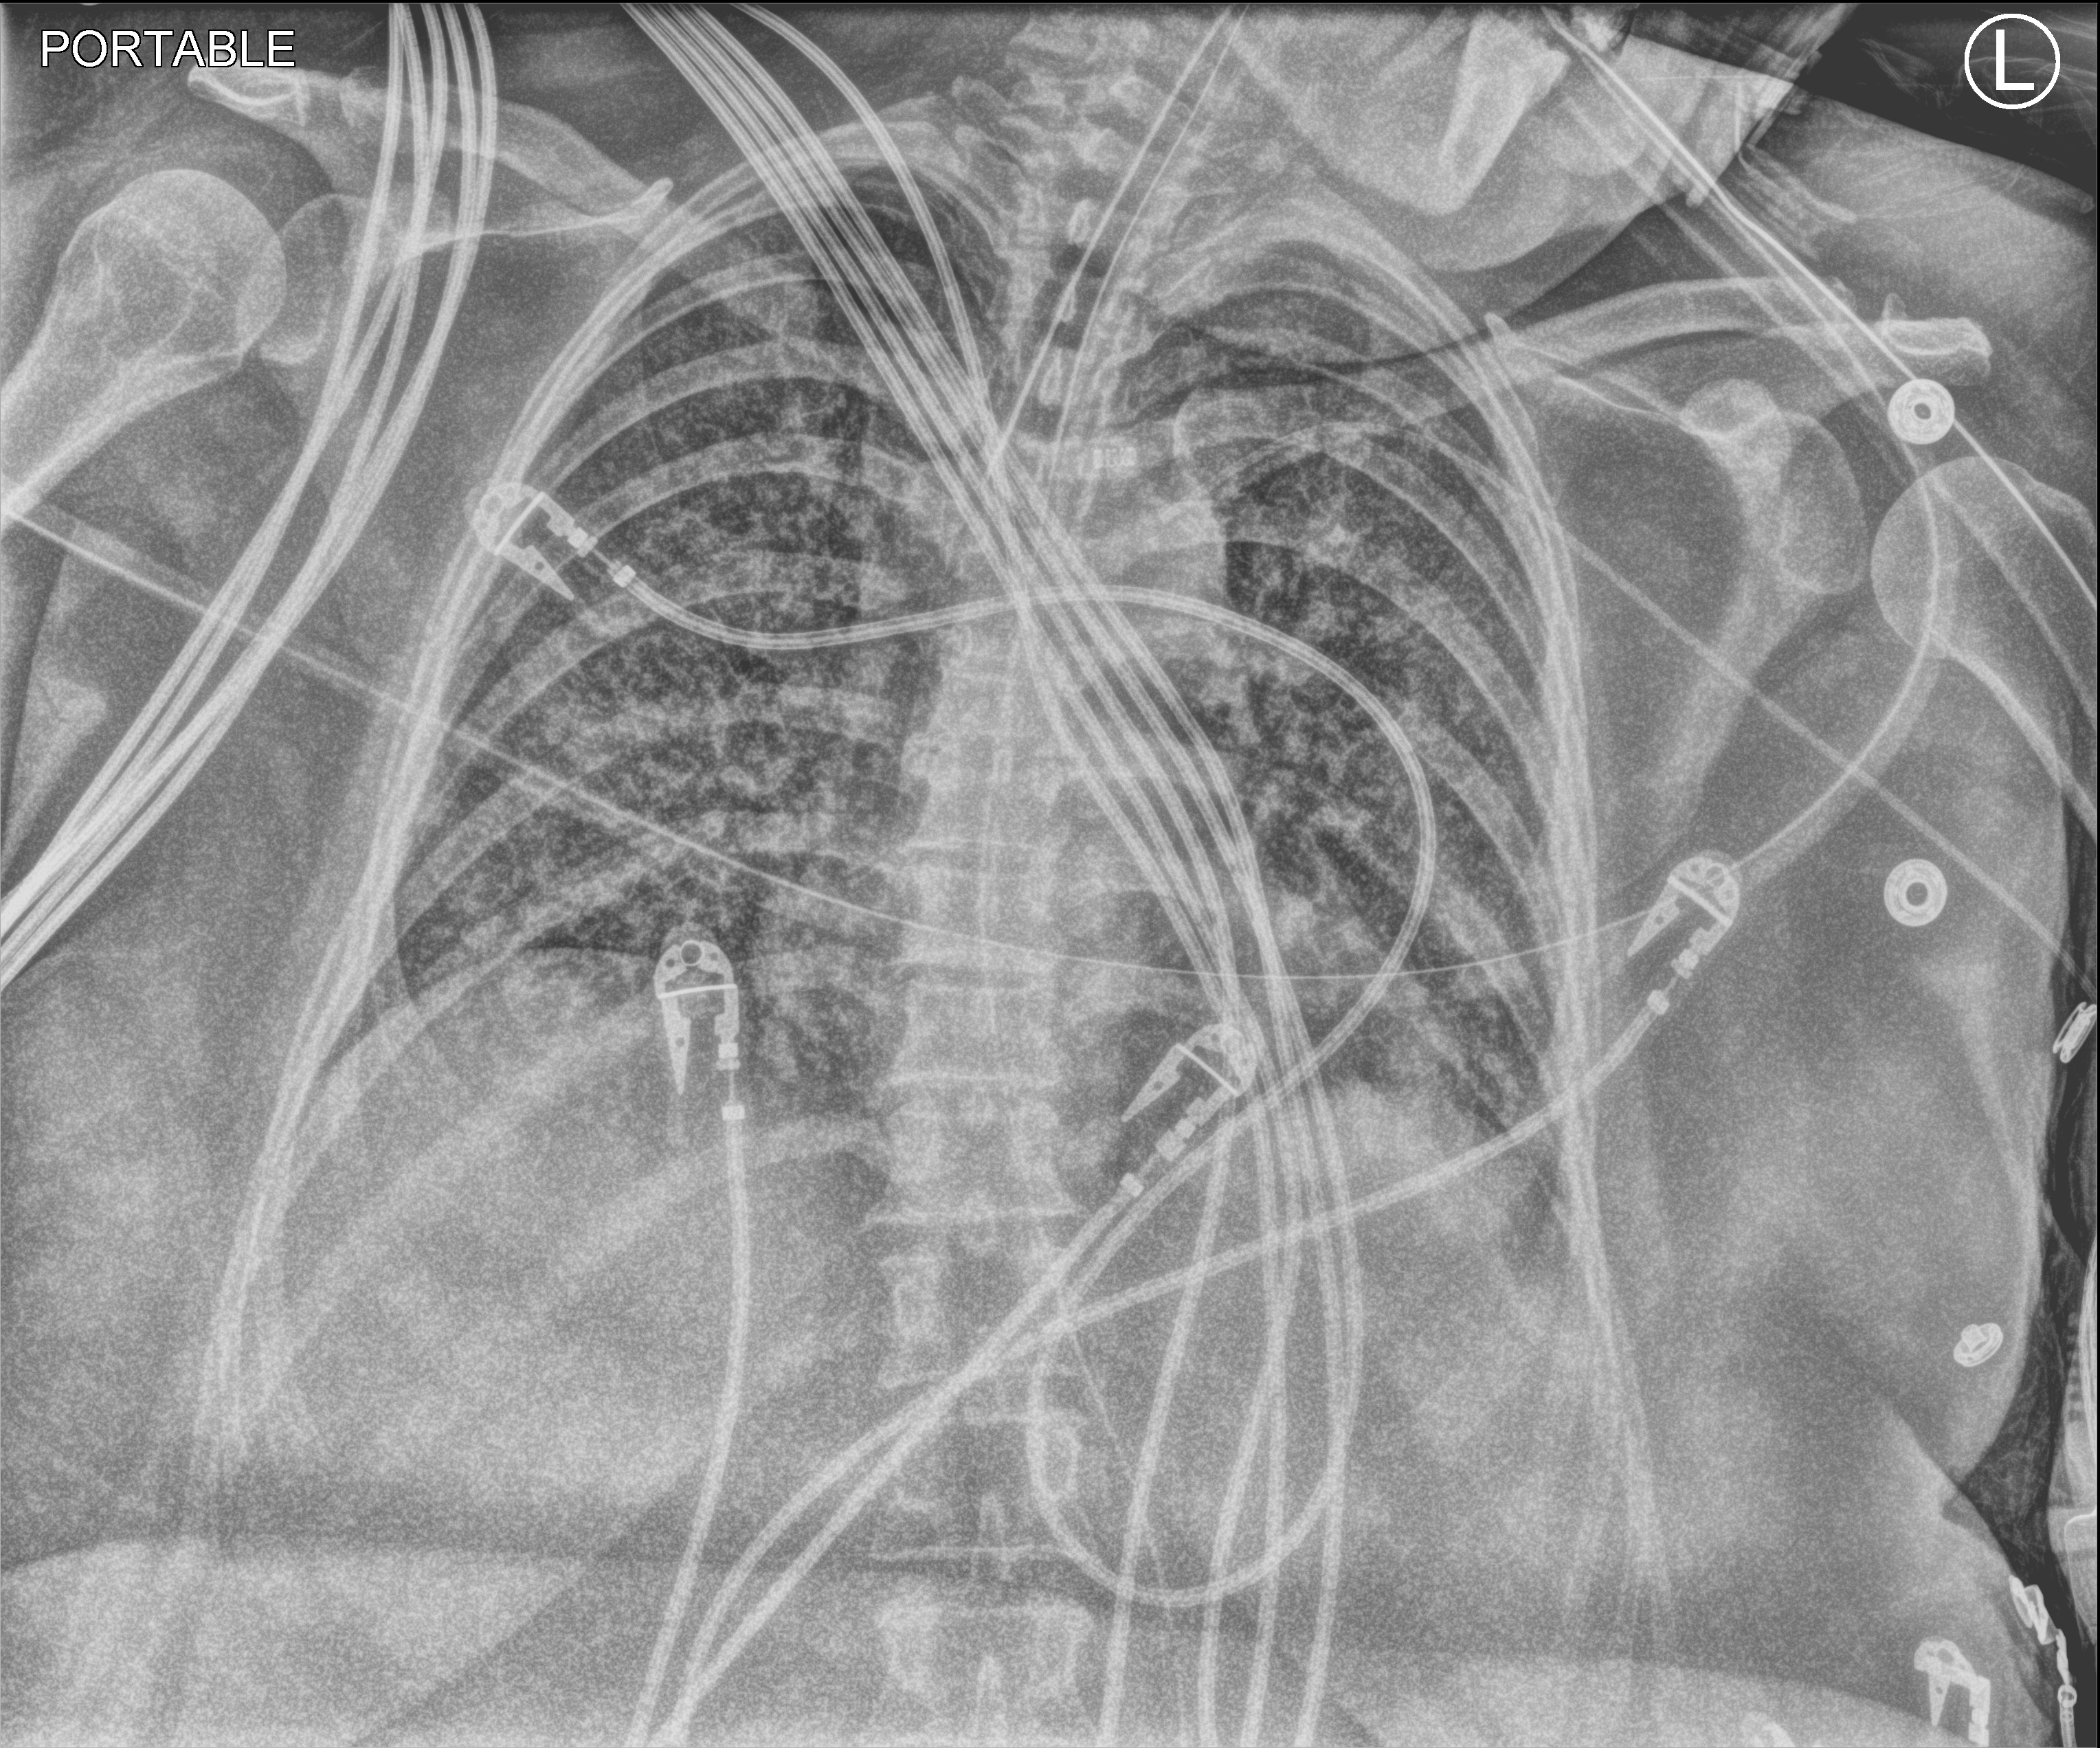
Chest X-ray (portable); anteroposterior (AP) projection. Patient hospitalised with COVID-19; female, aged 18–59 years.
Hospital-stay facts (about this admission, not read from this image; timing relative to this image not recorded):
- diabetes (admission record): no
- admitted to intensive care during this hospital stay: yes